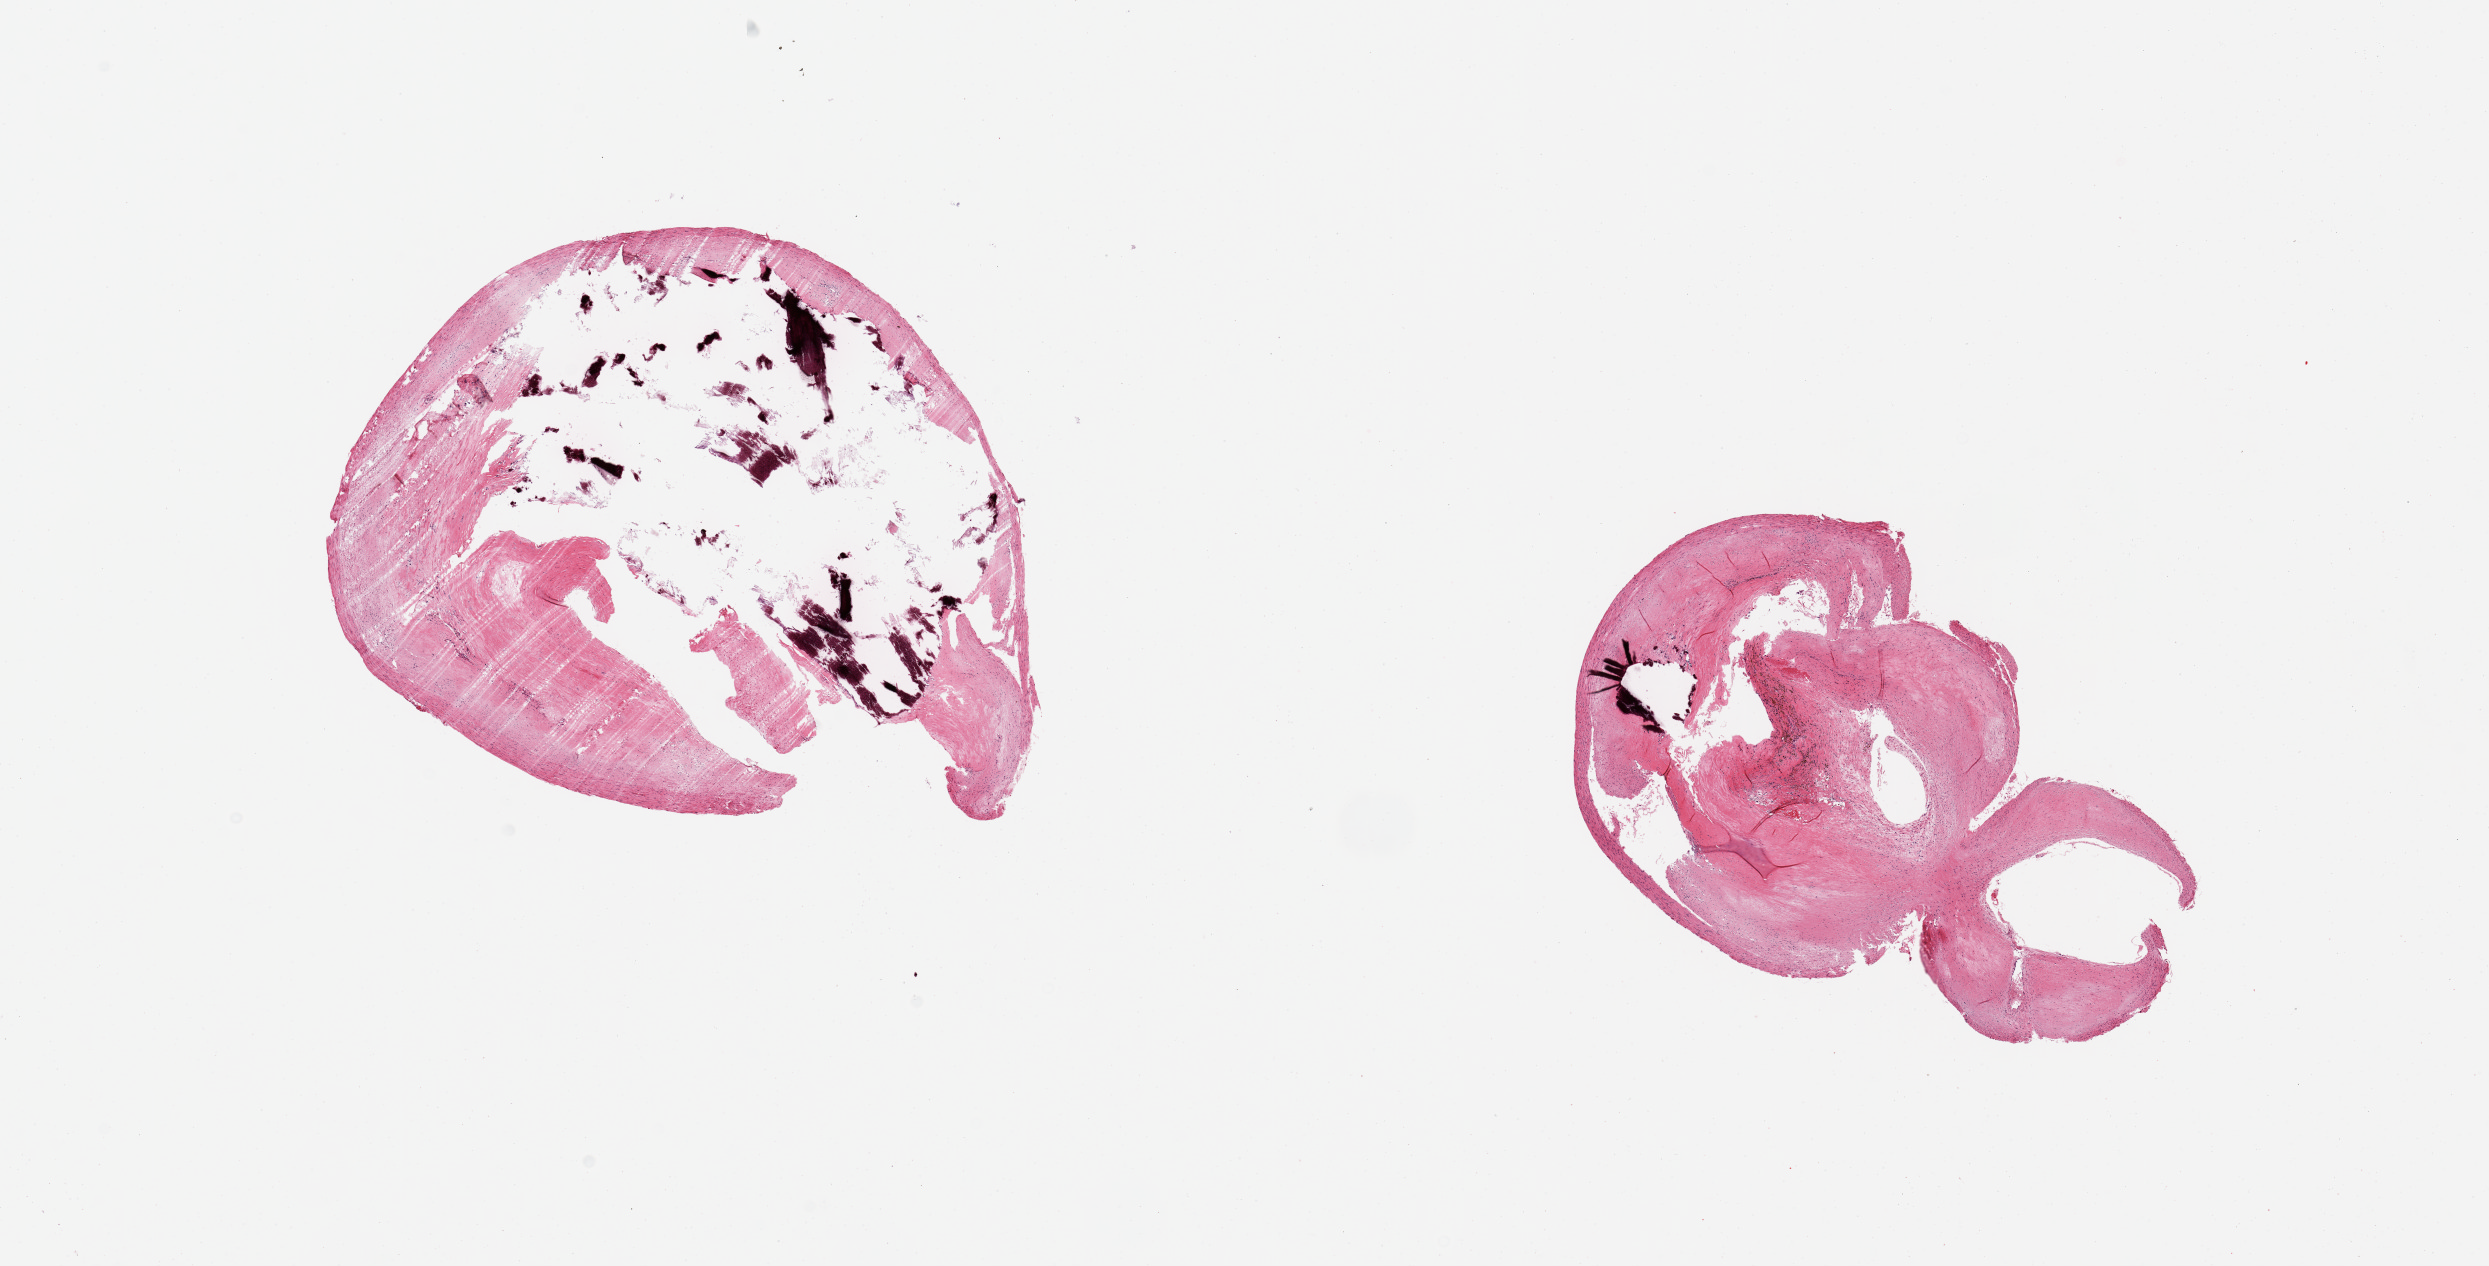
Digitized haematoxylin and eosin-stained section — whole scanned area (about 19.7 x 10.0 mm, acquisition: 20x scan) shown as a low-resolution overview; PAXgene-fixed paraffin-embedded (PFPE) section; target tissue: coronary artery; donor tissue sample.
Reviewer comment on this tissue sample: 2 pieces; Severe calcific atherosclerosis with organized thrombus and luminal compromise.